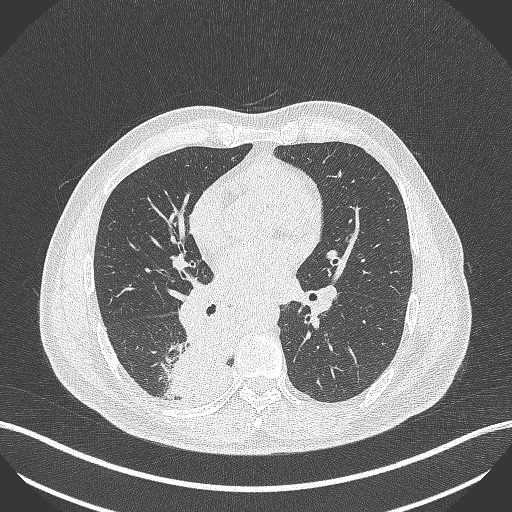
Chest CT, one axial slice; position 233 of 451 along the scan axis; 100 kVp; lung window (W 1500 / L -600 HU); 512 × 512 image matrix, field of view 400 × 400 mm. Patient: male, 61 years. Case-level facts recorded for this patient, not image findings: clinical TNM (as recorded): T1 N0 M0; histopathological grade: G3.
Annotated regions visible in this slice (rectangle marked by the reading radiologist):
- lung tumour (recorded histology: small cell carcinoma): box from (x=162, y=310) to (x=236, y=398) px